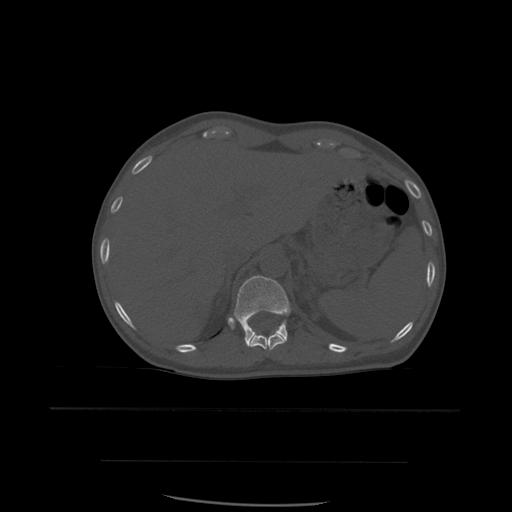
CT including the spine, one axial slice; position 284 of 574 along the scan axis; bone window (W 1800 / L 400 HU); 1.25 mm slice thickness; 512 × 512 image matrix, field of view 392 × 392 mm. Patient age 48 years. From the clinical record (not read from this slice): primary cancer: lung; vertebrae with lytic lesions (as recorded): T11.
Structures marked on this image (semi-automatic segmentation, software-assisted and operator-edited):
- T11 vertebra: bounding box [x1, y1, x2, y2] px = [250, 331, 287, 351]
- T12 vertebra: [233, 276, 291, 347]